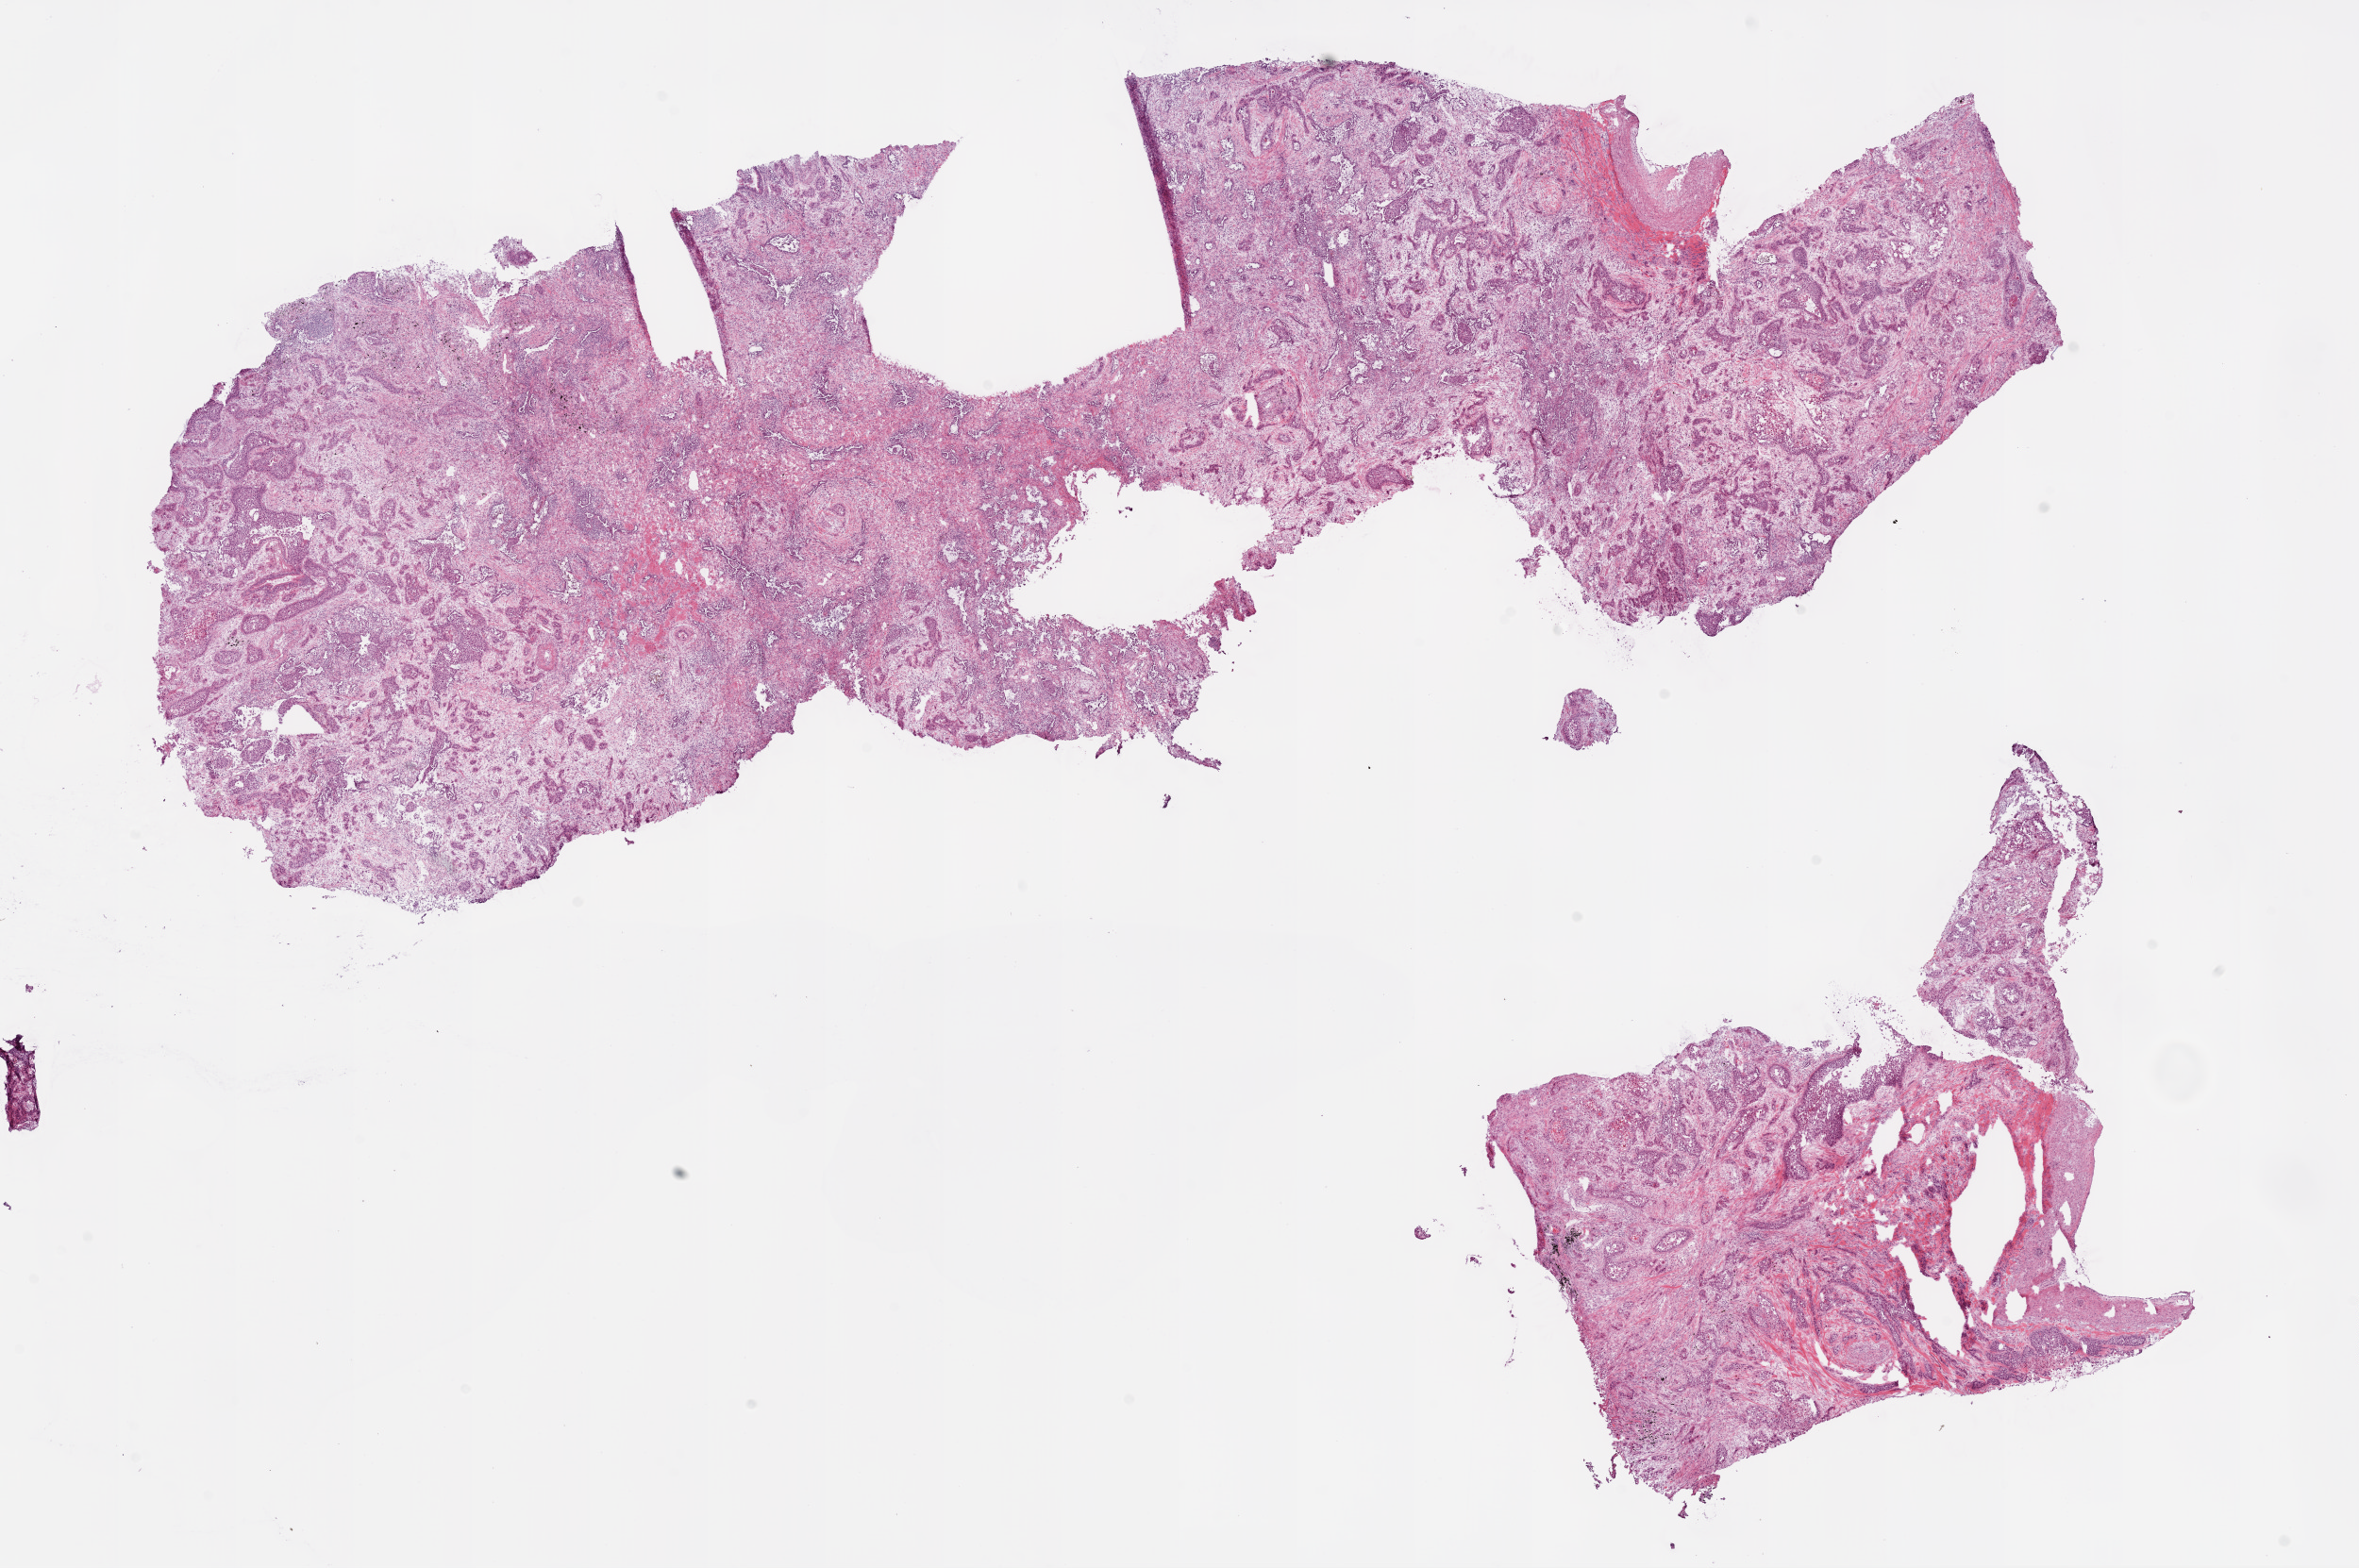
Hematoxylin and eosin (H&E) stained whole-slide image — a low-resolution overview of the entire scanned area, about 20.1 x 13.3 mm (slide scanned at 20x). Frozen section from the bottom of the tissue portion. Lung, primary tumour sample. Patient: male, age at initial diagnosis 76 years. Composition of this section per pathologist review: tumour cells 55%, tumour nuclei 70%, normal cells 0%, stromal cells 40%, necrosis 5%.
* histologic diagnosis: Squamous cell carcinoma, NOS
* AJCC pathologic stage: IIA